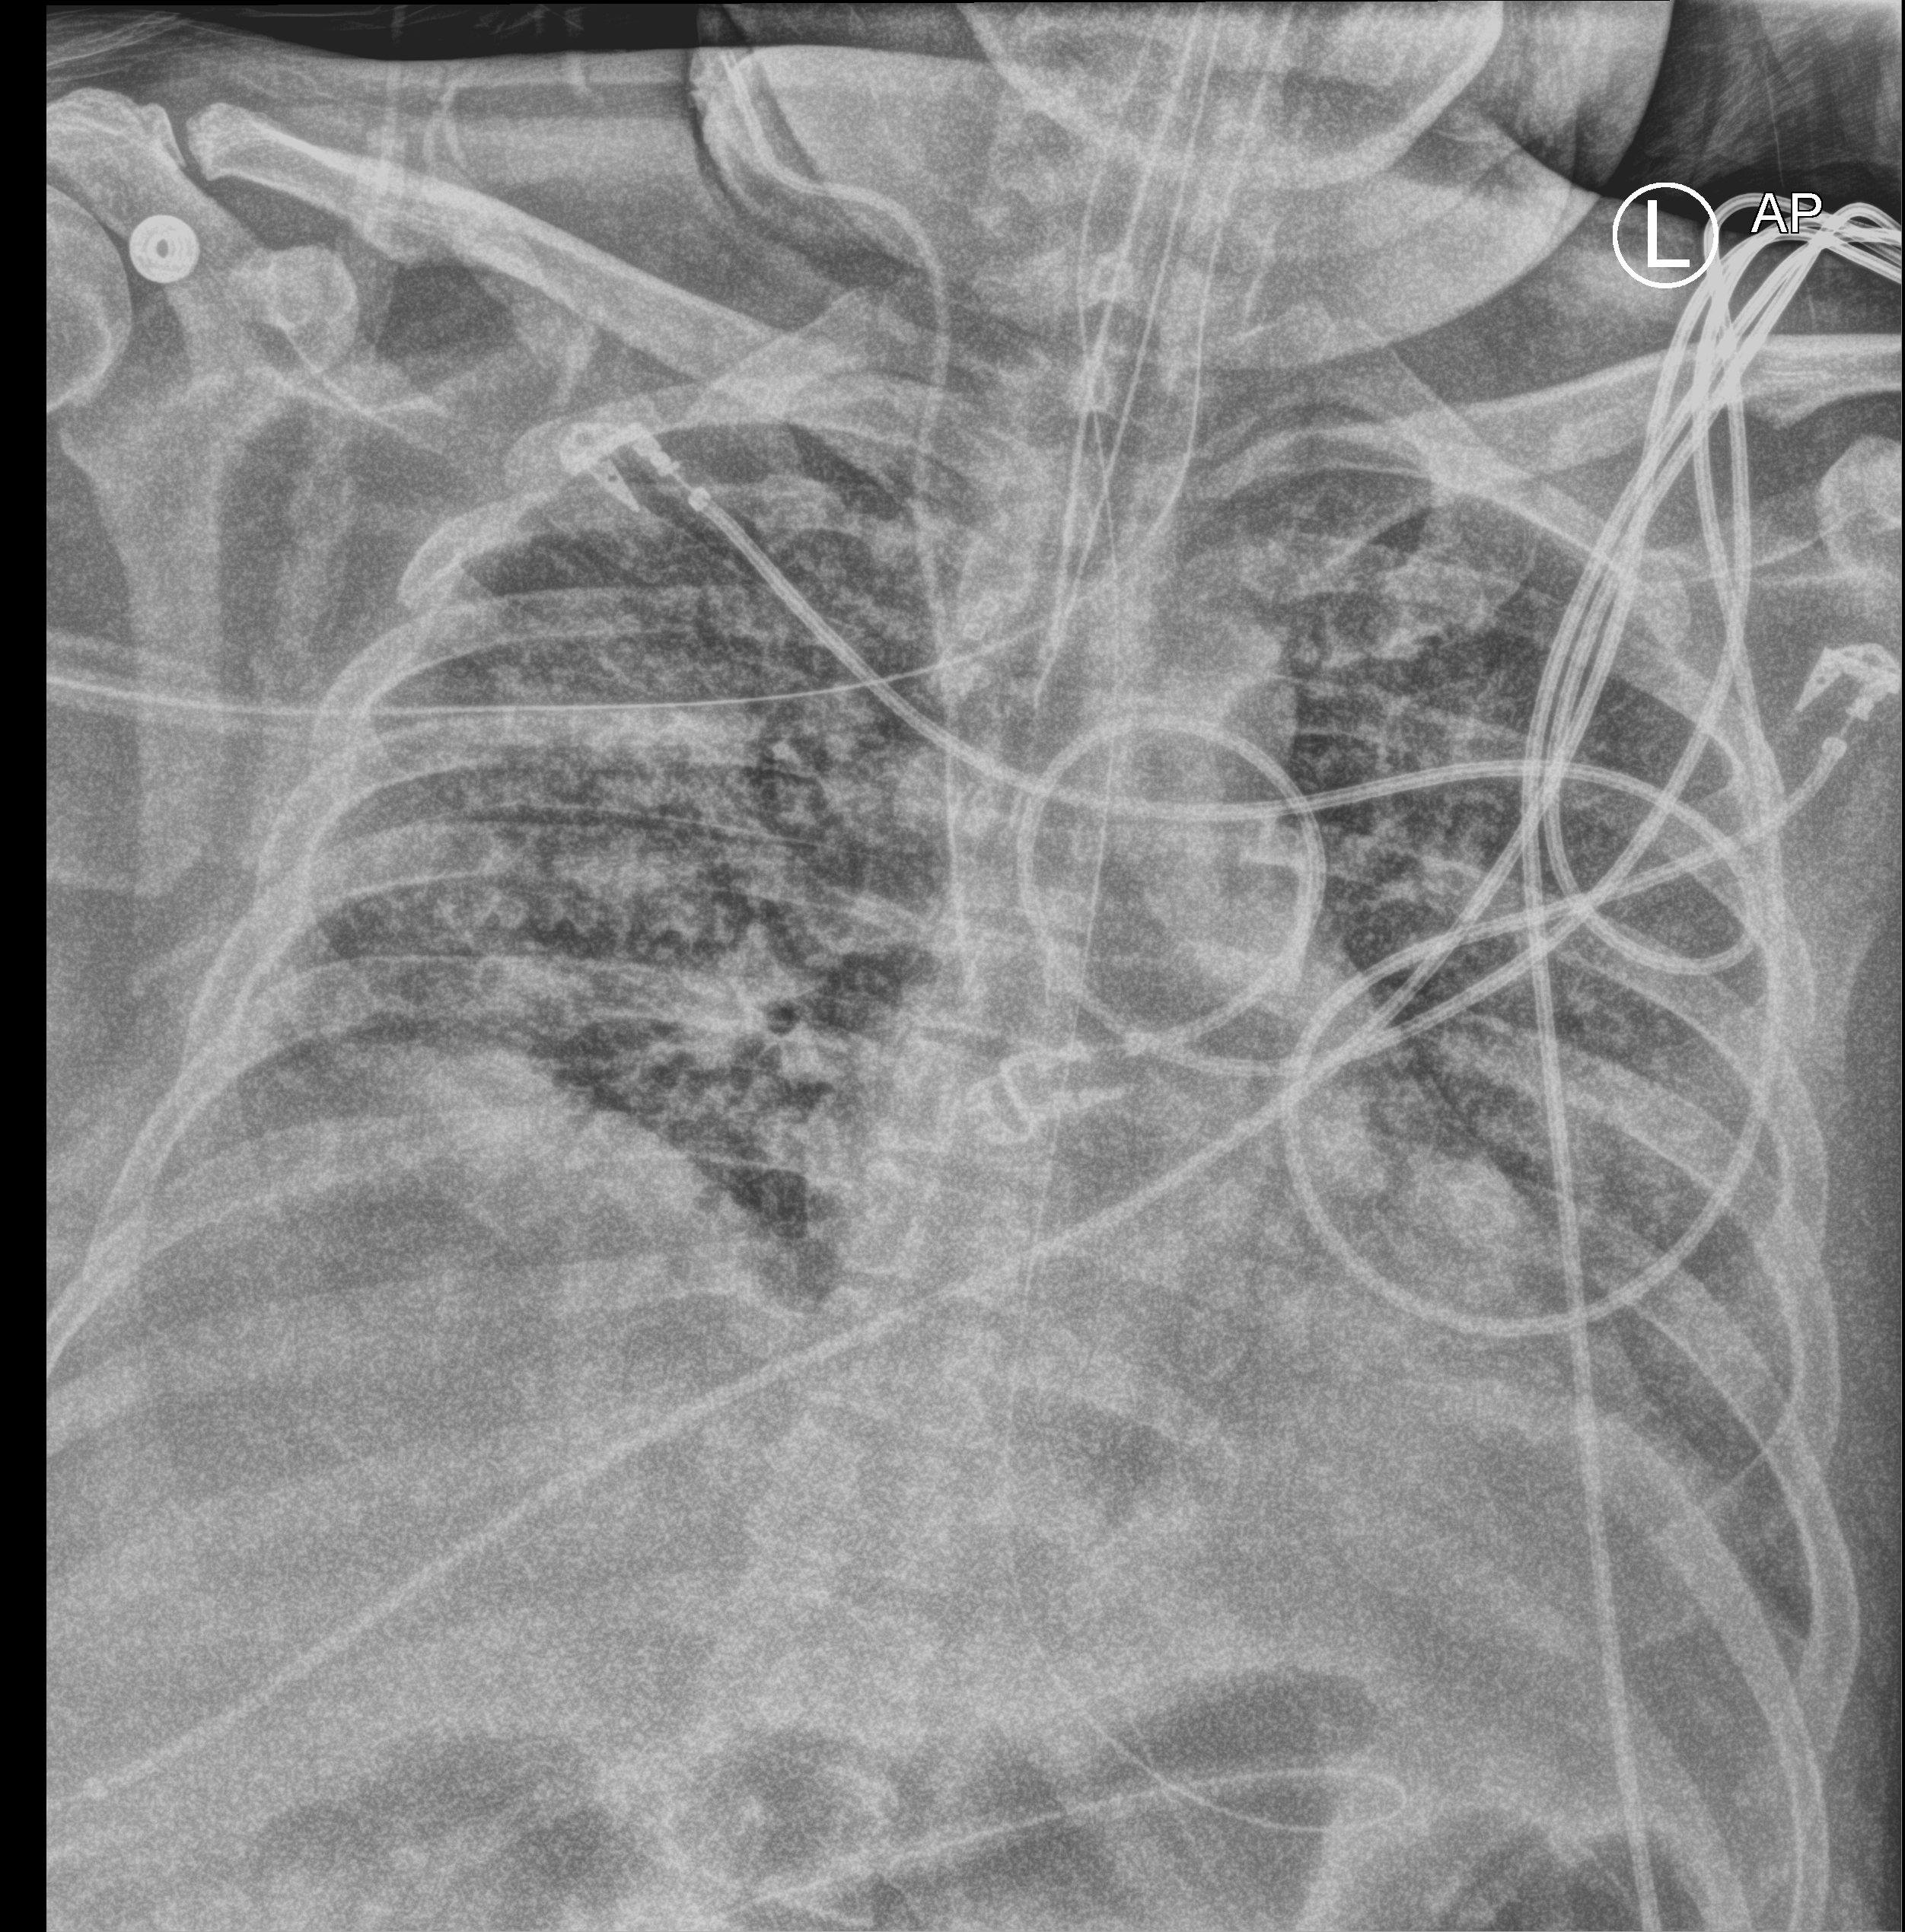
Bedside chest radiograph (computed radiography), anteroposterior (AP) projection. Patient hospitalised with COVID-19; male, aged 18–59 years.
Hospital-stay facts (about this admission, not read from this image; timing relative to this image not recorded):
- mechanically ventilated during this hospital stay: yes